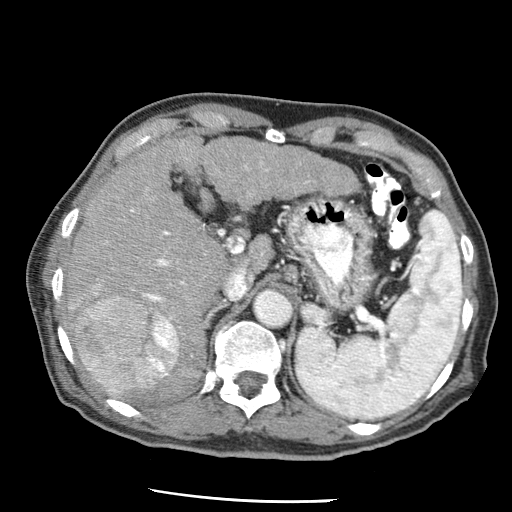
Contrast-enhanced abdominal CT (liver protocol), one axial slice; slice 36 of 79 in the series (ordered by position); 120 kVp; soft-tissue window (W 400 / L 40 HU); 2.5 mm slice thickness; 512 × 512 image matrix, field of view 320 × 320 mm. From the clinical record (not read from this slice): diagnosis: hepatocellular carcinoma (patient treated with transarterial chemoembolisation; whether this scan precedes or follows treatment is not stated here); TNM stage (as recorded): Stage-IIIA; Child-Pugh class: A; tumour differentiation: moderately differentiated; tumour size: 7 cm.
Annotated regions visible in this slice (semi-automatic segmentation, software-assisted and operator-edited):
- liver parenchyma outside the tumour (the mass and vessels are separate outlines, so this box may not span the whole liver): bounding box <64,138,358,396> (left, top, right, bottom; pixels)
- mass: <70,295,178,392>
- liver vessels: <70,166,308,393>